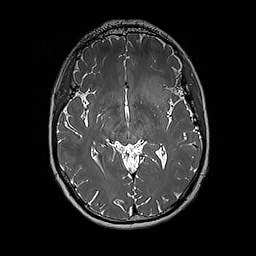
Brain MRI from a brain-tumour surgery series, one axial slice. Slice 105 of 192 in the series (ordered by position). 1 mm slice thickness. 256 × 256 image matrix, field of view 250 × 250 mm. Case-level facts recorded for this patient, not image findings: histopathology: Glioblastoma; WHO grade: 4; IDH mutation: no; tumour location: Left Insular.
Structures marked on this image (outlined manually by an expert reader):
- tumour: box from (x=140, y=76) to (x=171, y=113) px